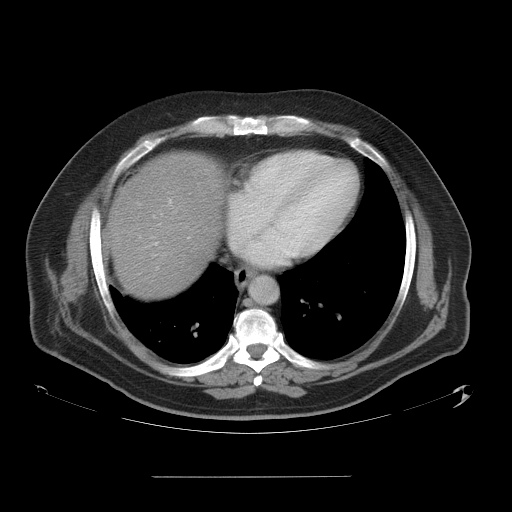
Contrast-enhanced abdominal CT, one axial slice. Slice 52 of 58 in the series (ordered by position). Intravenous contrast given. Soft-tissue window (W 400 / L 40 HU). 5 mm slice thickness. 512 × 512 image matrix. Male patient, age 63 years. From the clinical record (not read from this slice): diagnosis: colorectal cancer liver metastases, imaged before liver resection; multiple liver metastases: no; largest metastasis: 4.2 cm; disease in both lobes: no.
Annotated regions visible in this slice (expert manual segmentation):
- hepatic veins: bounding box [x1, y1, x2, y2] px = [153, 203, 246, 258]
- liver: [111, 153, 224, 299]
- planned liver remnant (the part of the liver to remain after resection): [111, 215, 210, 300]
- portal vein (with intrahepatic branches): [169, 200, 172, 204]